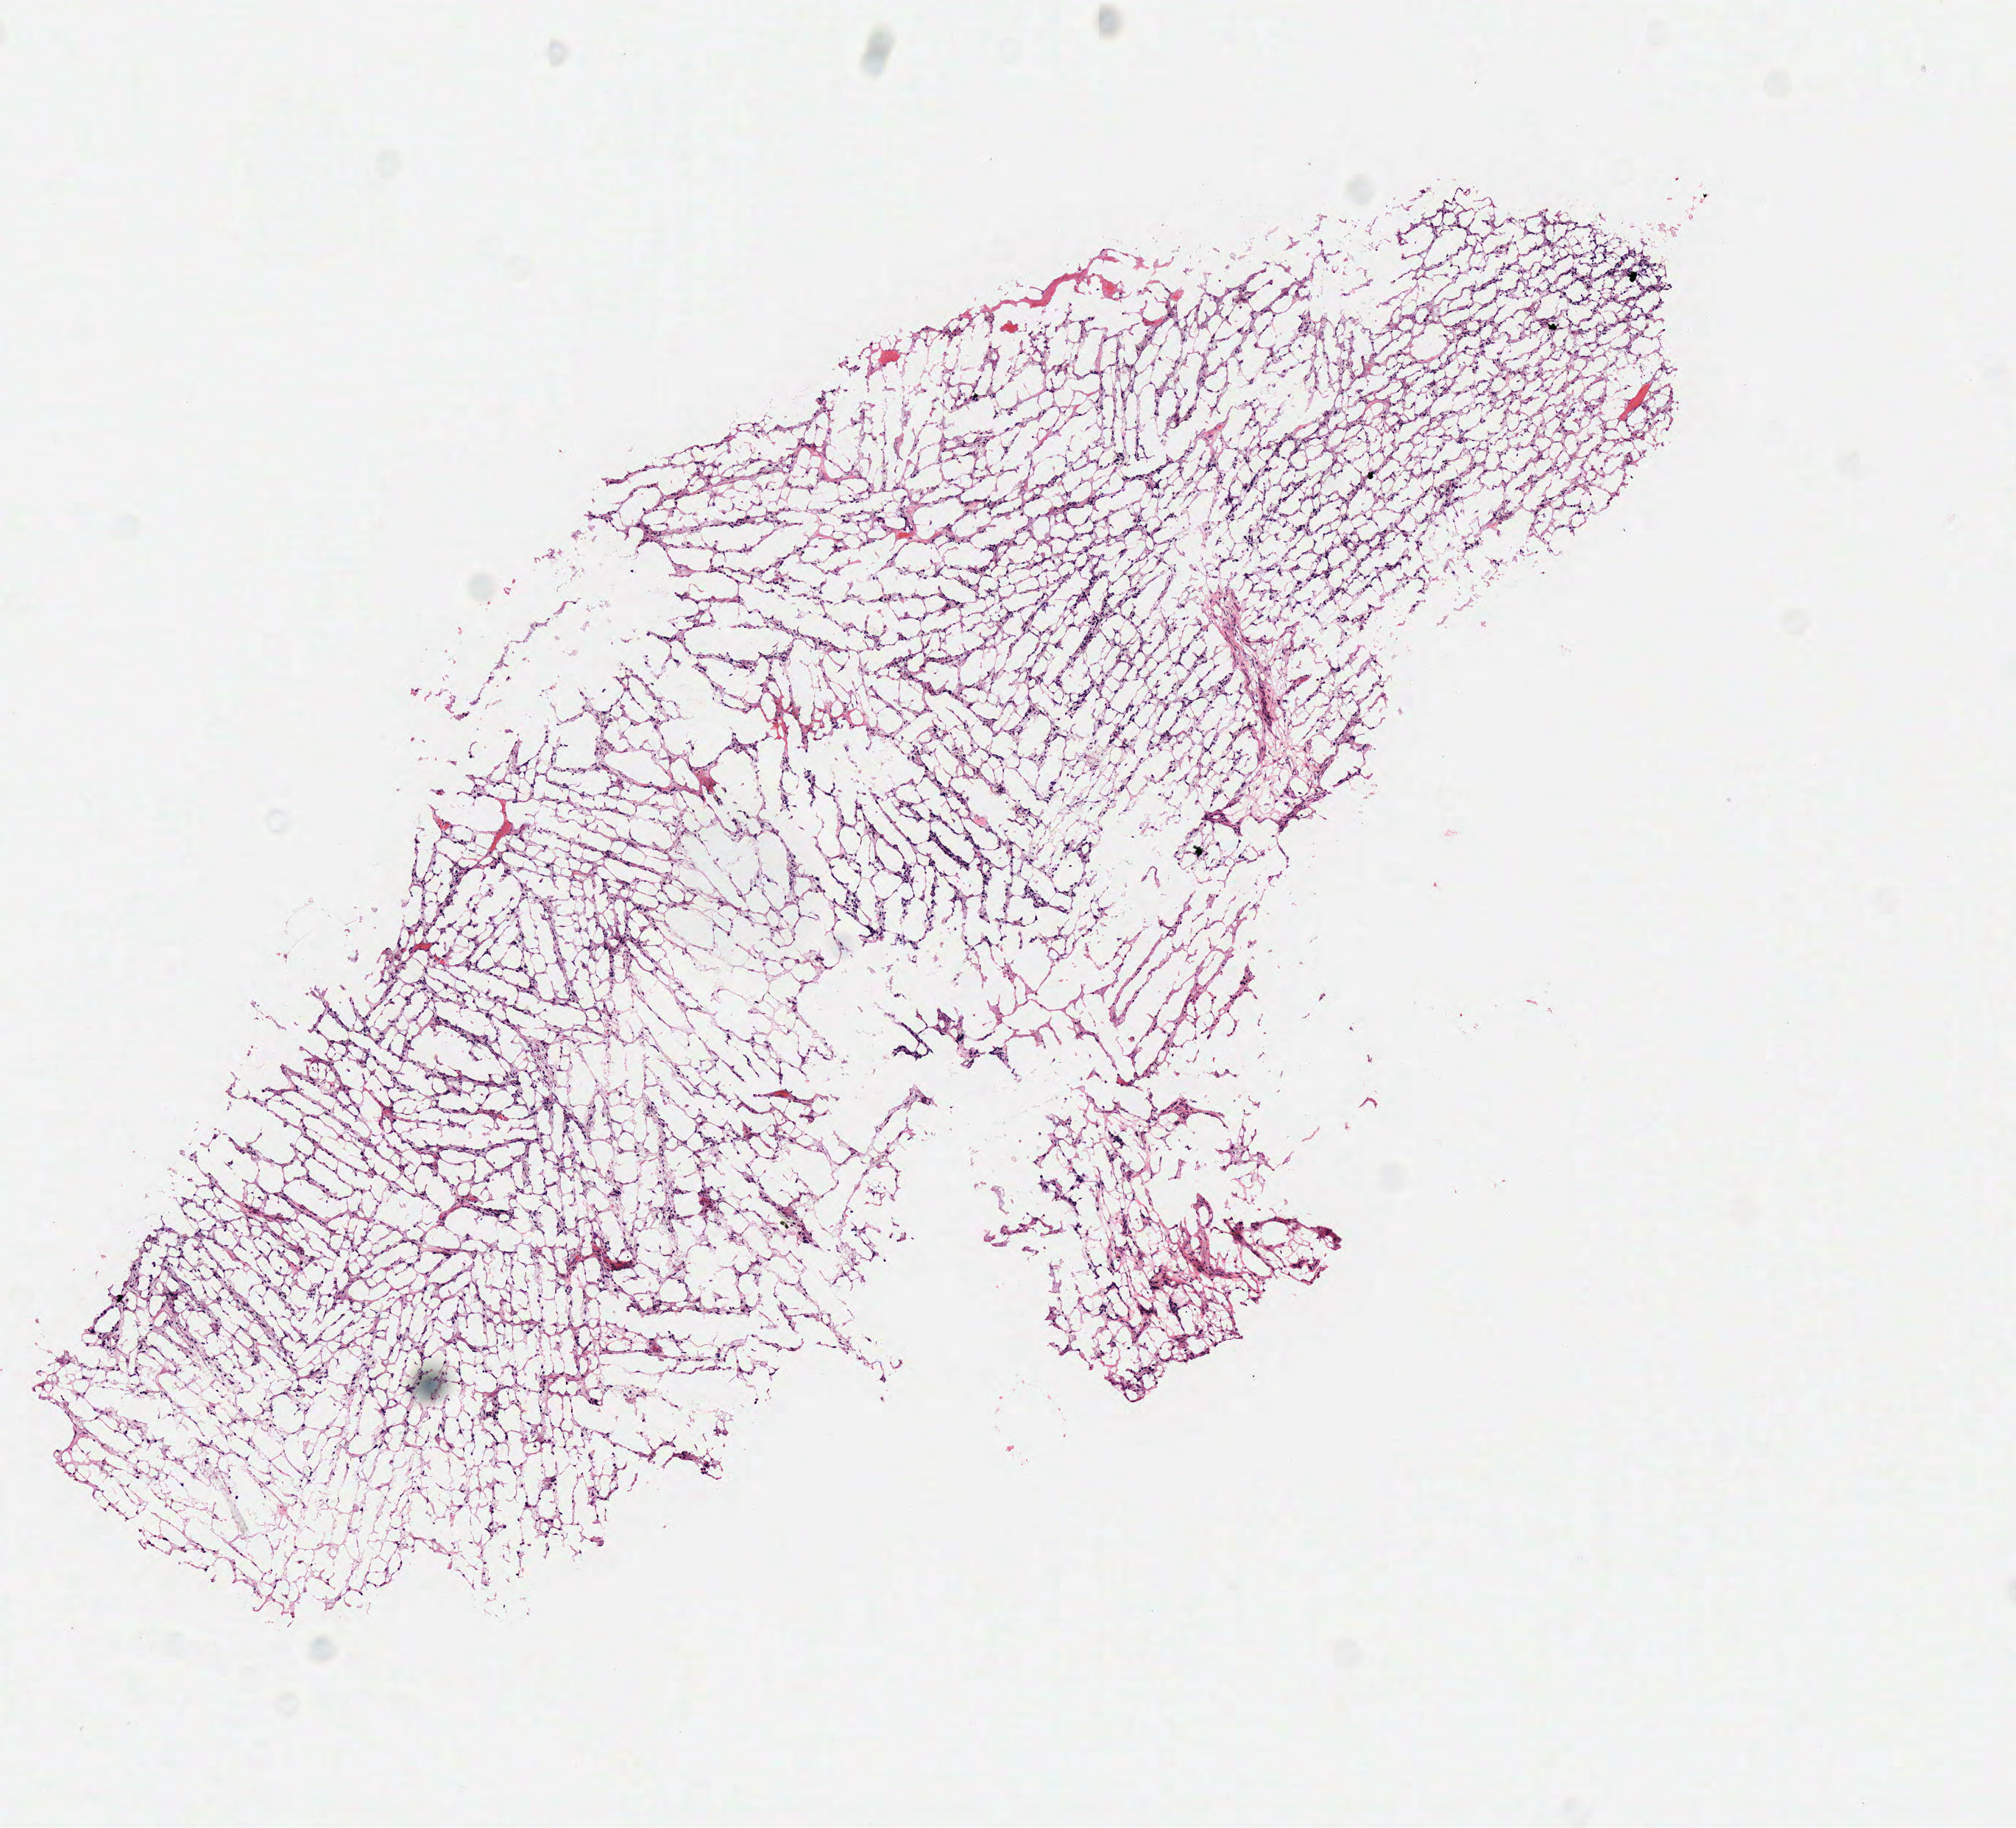
H&E whole-slide image — a low-resolution overview of the entire scanned area, about 5.4 x 4.9 mm (acquisition: 40x scan); frozen section from the top of the tissue portion; primary tumour sample from the brain. Patient: female, age at initial diagnosis 77 years. Composition of this section per pathologist review: tumour cells 100%, tumour nuclei 75%.
Histologic diagnosis: Glioblastoma.